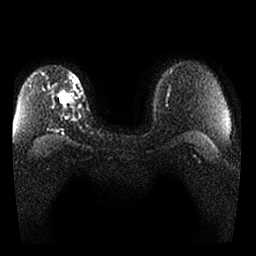
Breast MRI, one axial slice; diffusion-weighted series; image 2 of 4 stored at this slice position (different b-values; order by instance number); 1.5 T; 256 × 256 image matrix, field of view 340 × 340 mm. Female patient.
Structures marked on this image (outlined manually by an expert reader):
- tumour on diffusion-weighted imaging: bounding box [x1, y1, x2, y2] px = [59, 91, 71, 104]